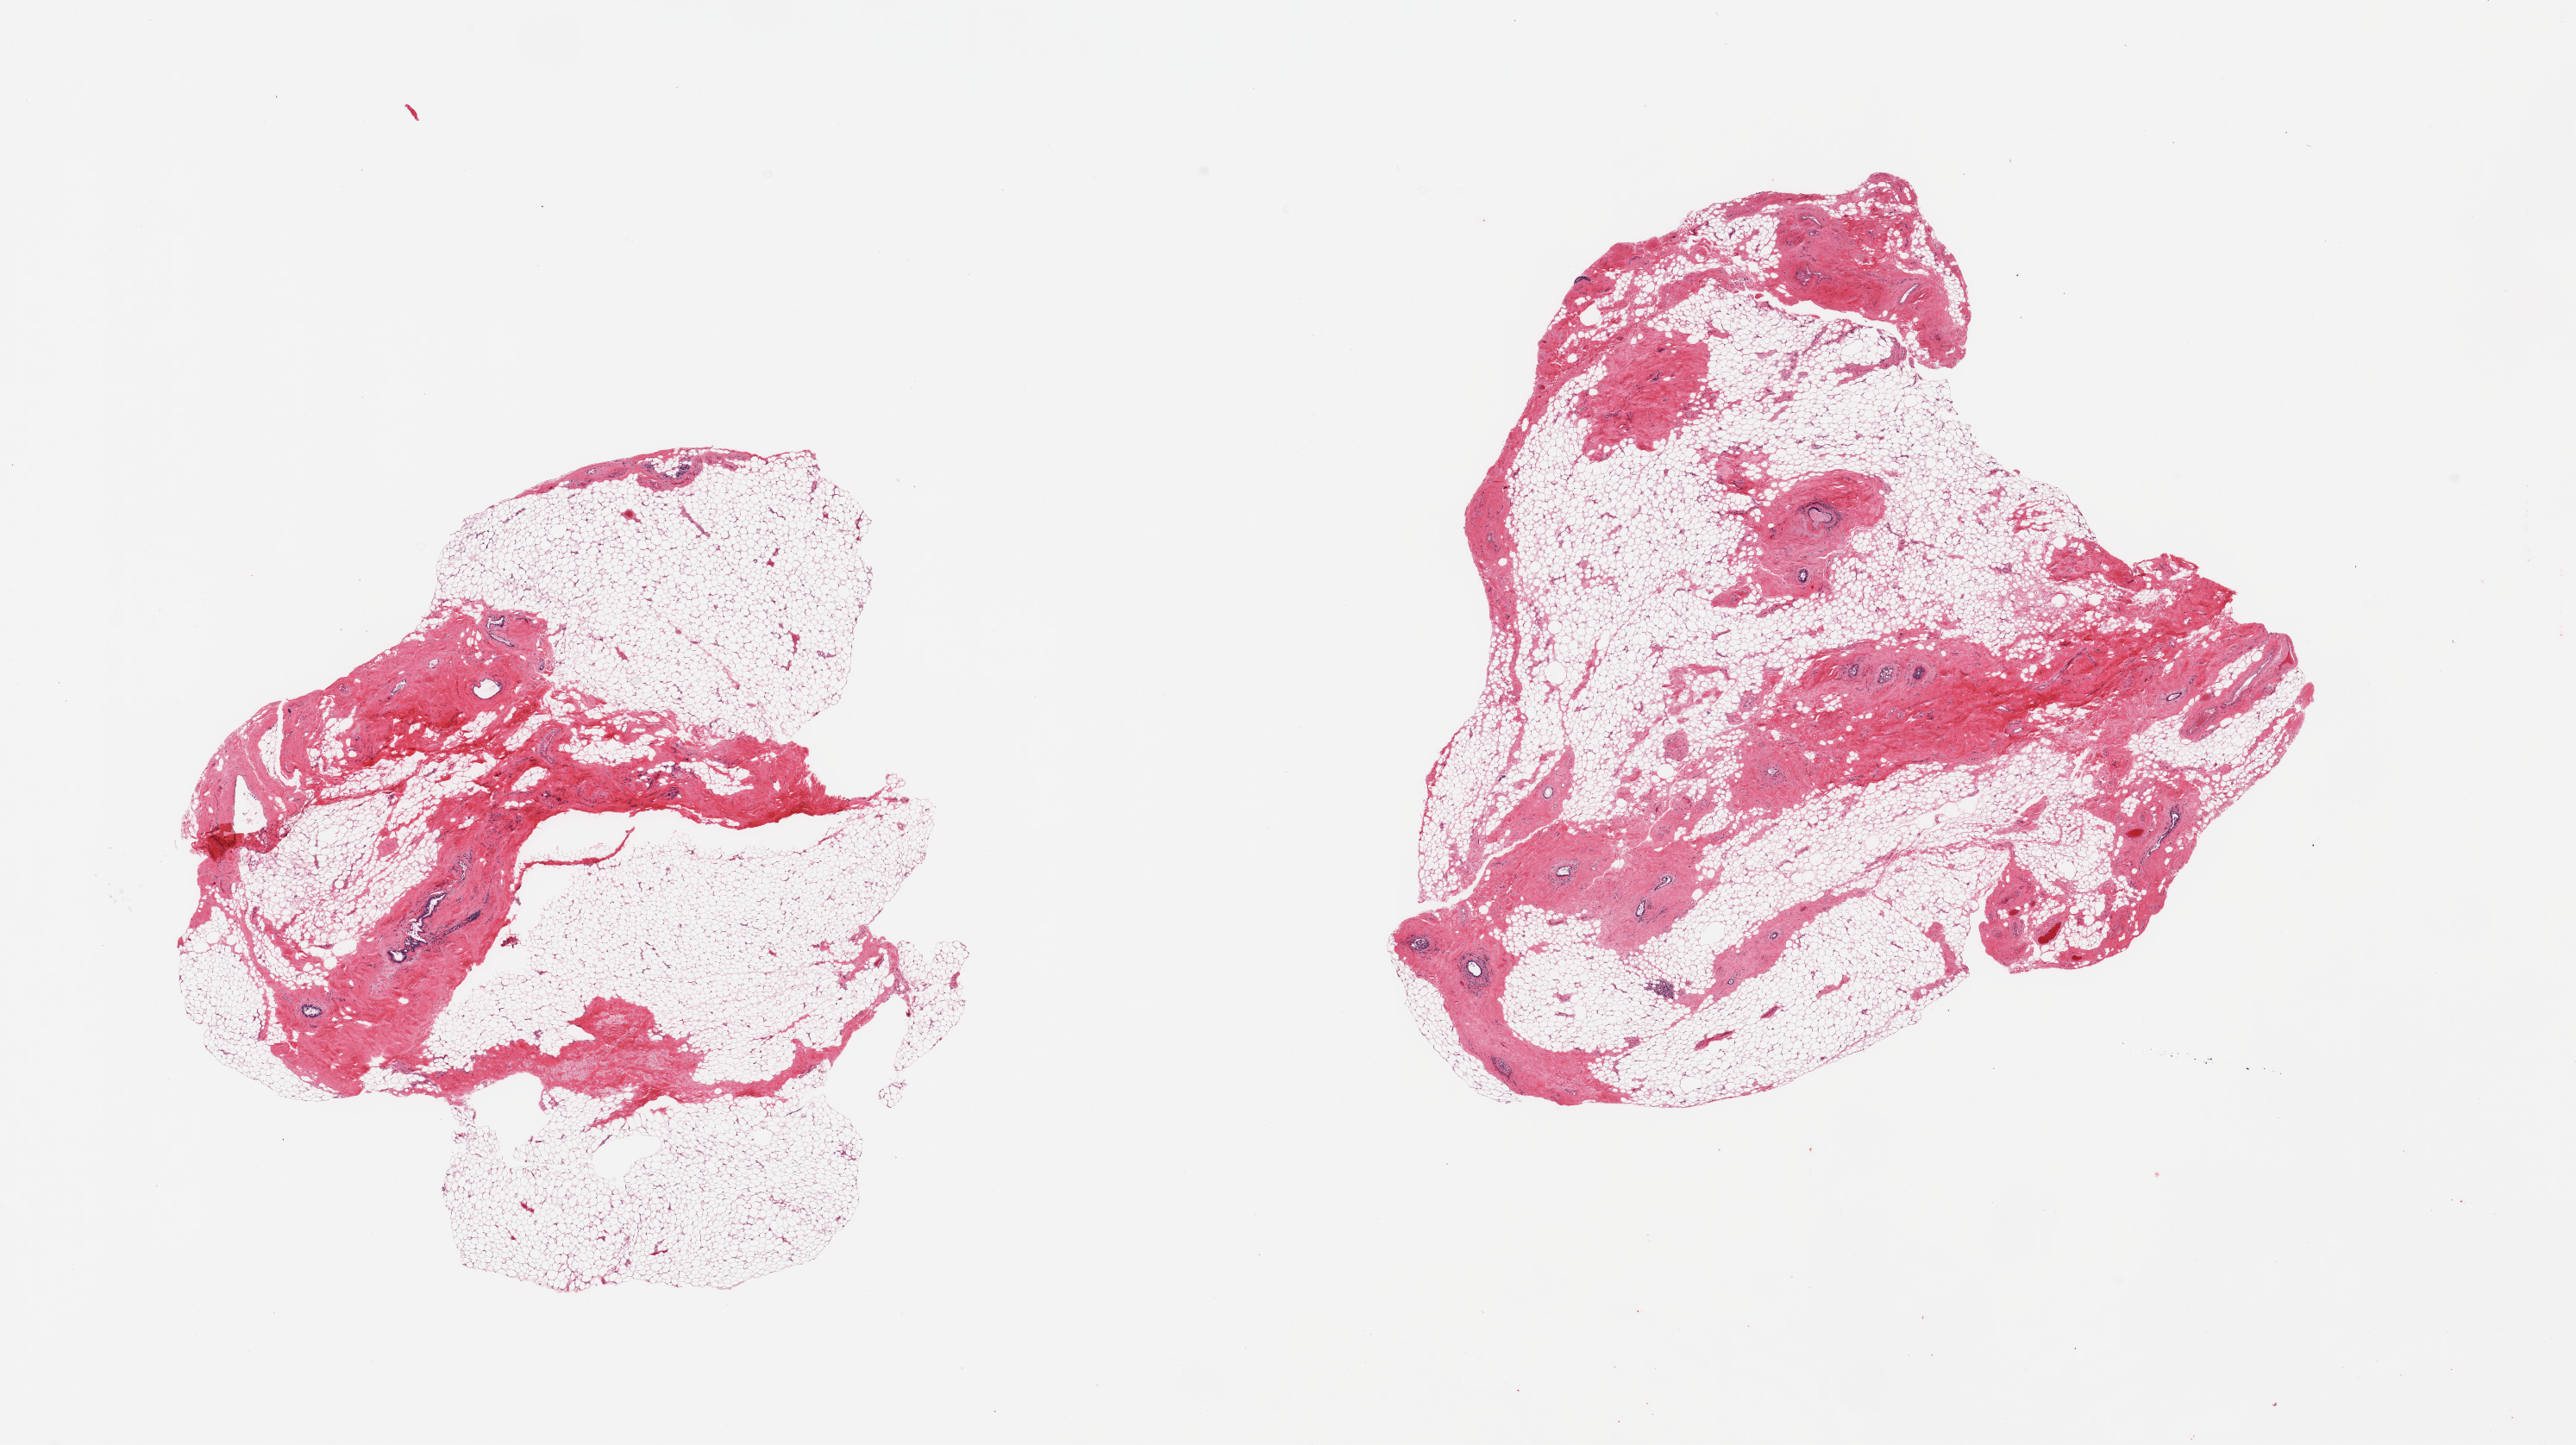
Digitized H&E-stained section, a low-resolution overview of the entire scanned area, about 23.6 x 13.3 mm. PAXgene-fixed, paraffin-embedded tissue. Section of breast (target tissue). Donor tissue sample. Donor sex: female.
Pathologist's review note for this sample: 2 pieces; atrophic ducts and lobules; 60% fat content.